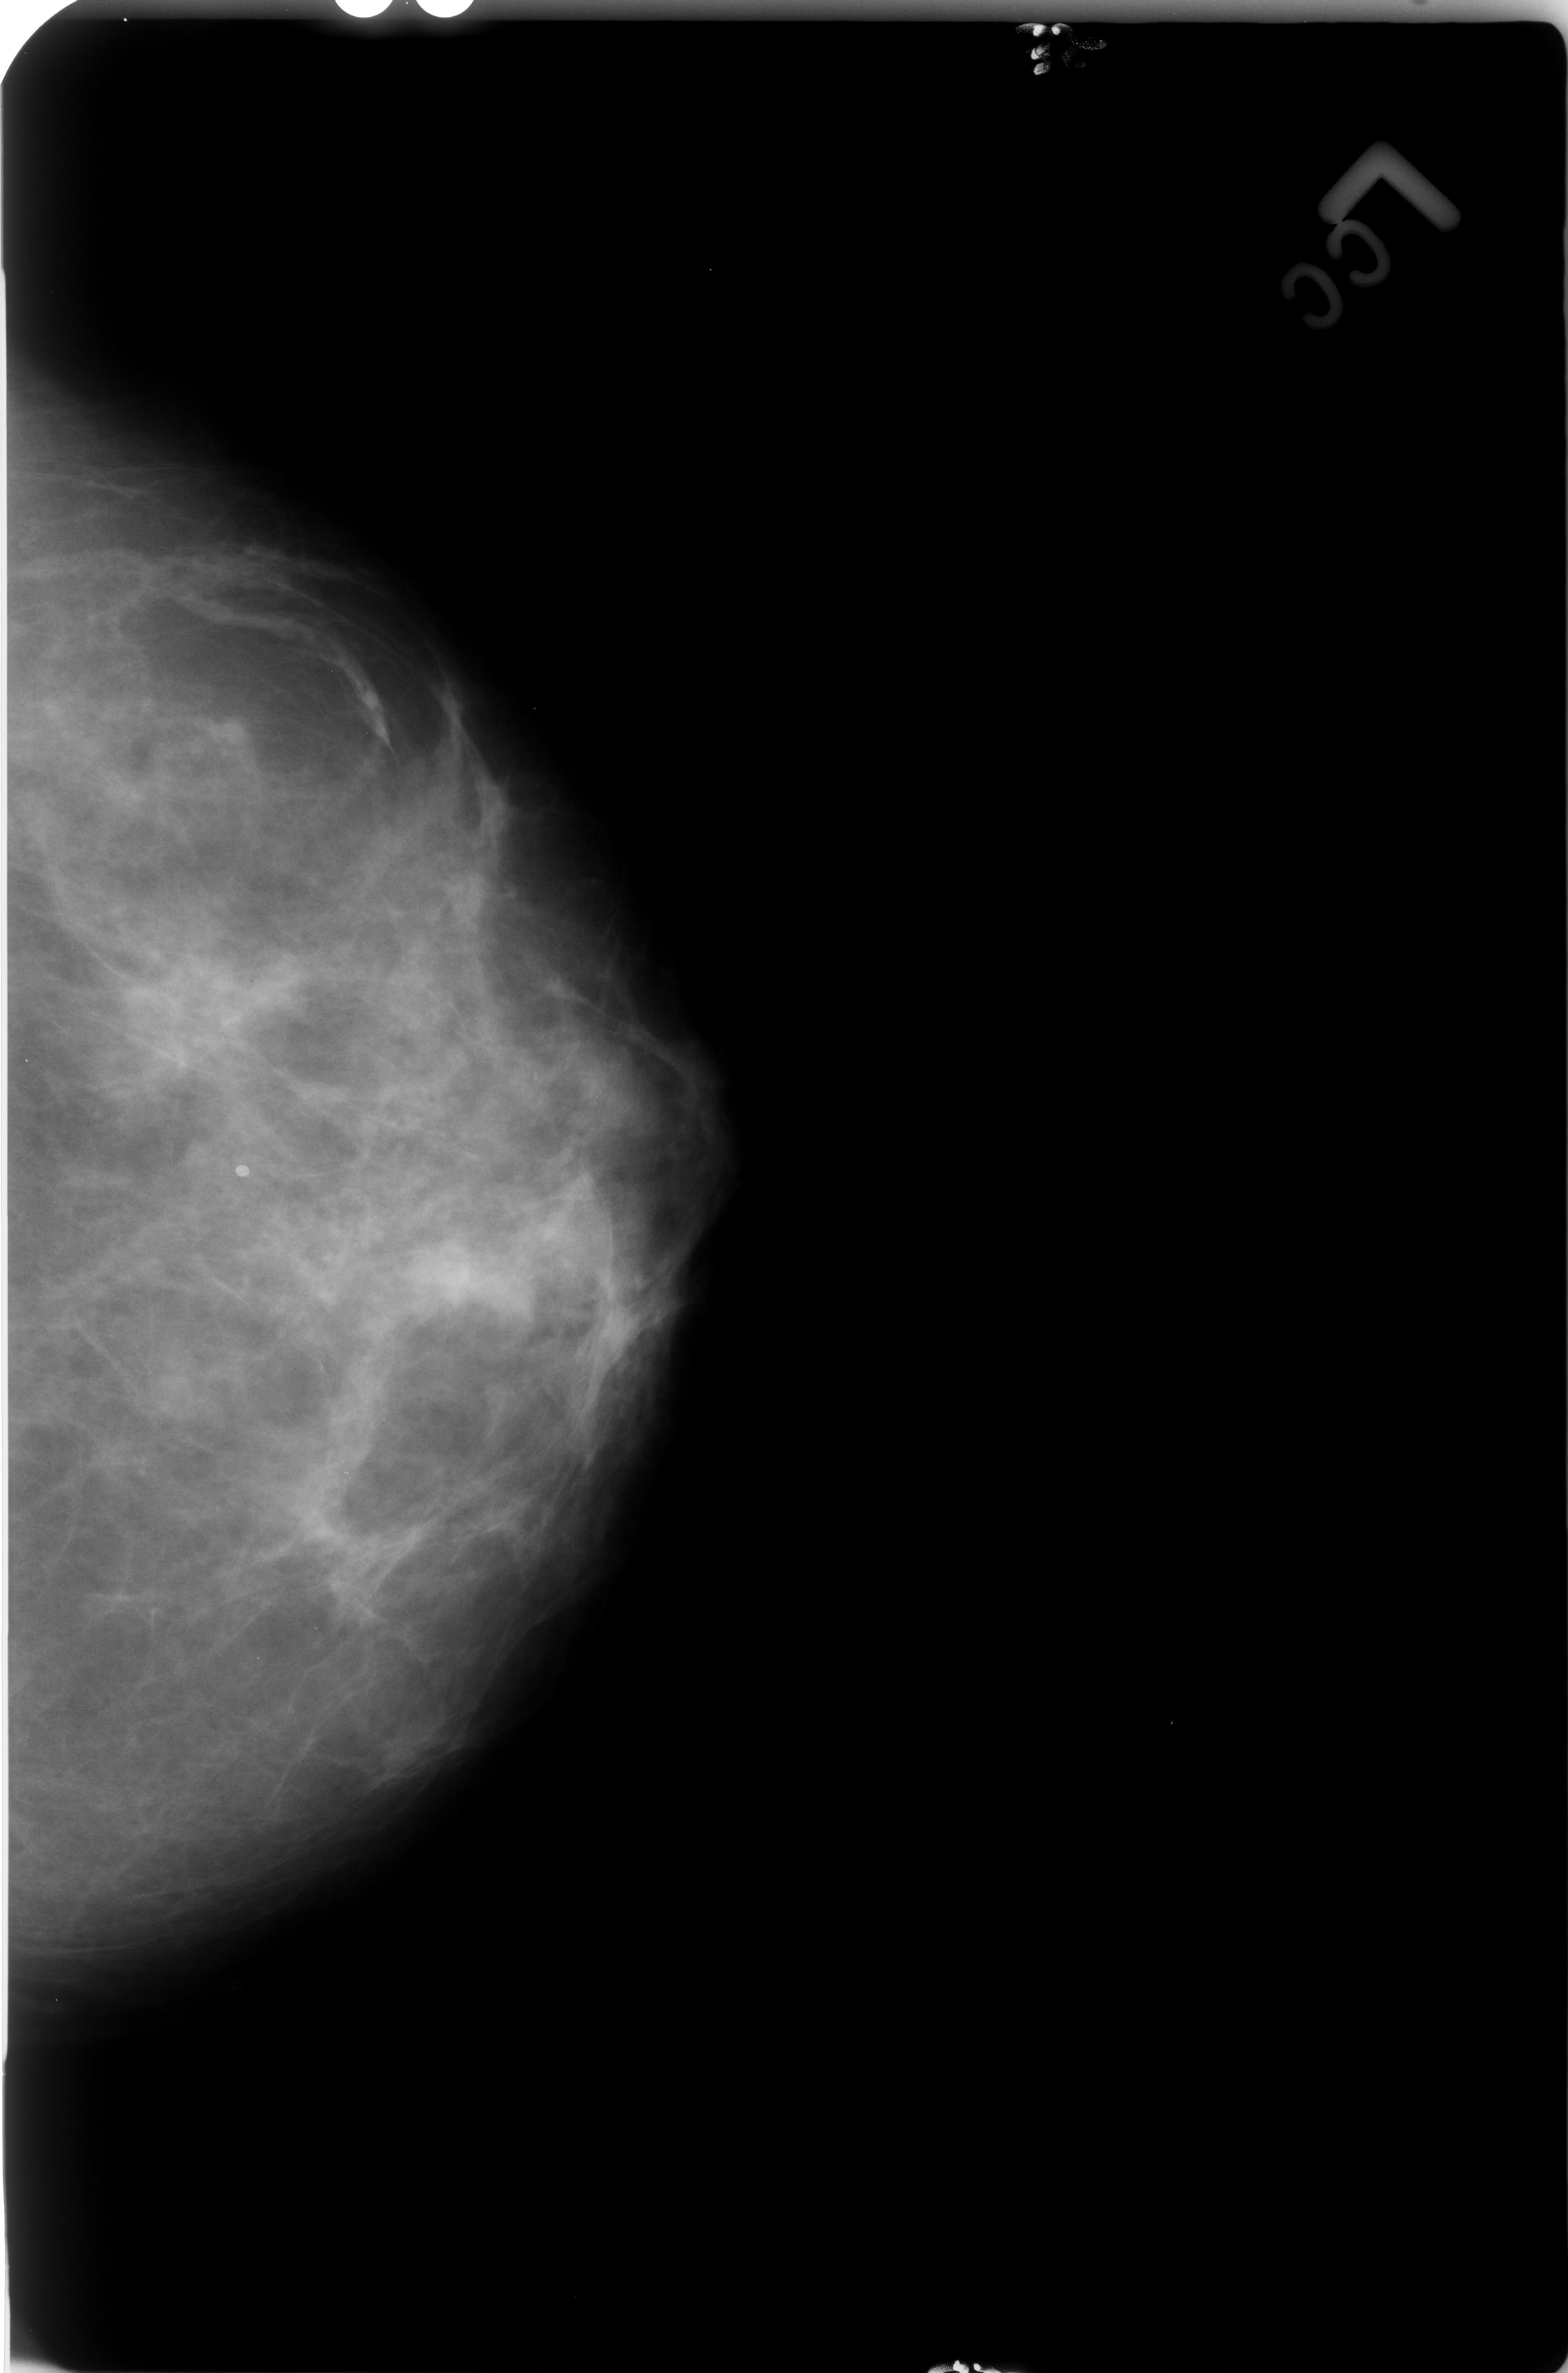
Scanned film-screen mammogram; left breast; craniocaudal (CC) view; 1568 × 2373 image matrix.
Expert-marked regions of interest on this image (one box per marked abnormality):
- calcifications, morphology lucent center; BI-RADS assessment category 2; subtlety rating 4 on a 1 (subtle) to 5 (obvious) scale; benign; no additional work-up was recommended (outcome (as recorded, no biopsy): benign without callback): box from (x=217, y=1133) to (x=280, y=1204) px